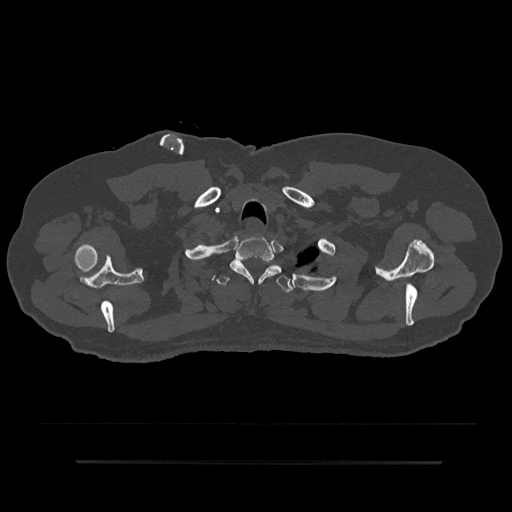
CT including the spine, one axial slice; position 726 of 797 along the scan axis; reconstruction kernel Br40s/3; 120 kVp; bone window (W 1800 / L 400 HU); 0.5 mm slice thickness; 512 × 512 image matrix, field of view 464 × 464 mm. Patient: male, 59 years. From the clinical record (not read from this slice): primary cancer: bile ducts.
Outlined on this slice (semi-automatic segmentation, software-assisted and operator-edited):
- T1 vertebra: box from (x=230, y=236) to (x=277, y=283) px
- T2 vertebra: (x=216, y=264)–(x=292, y=293)